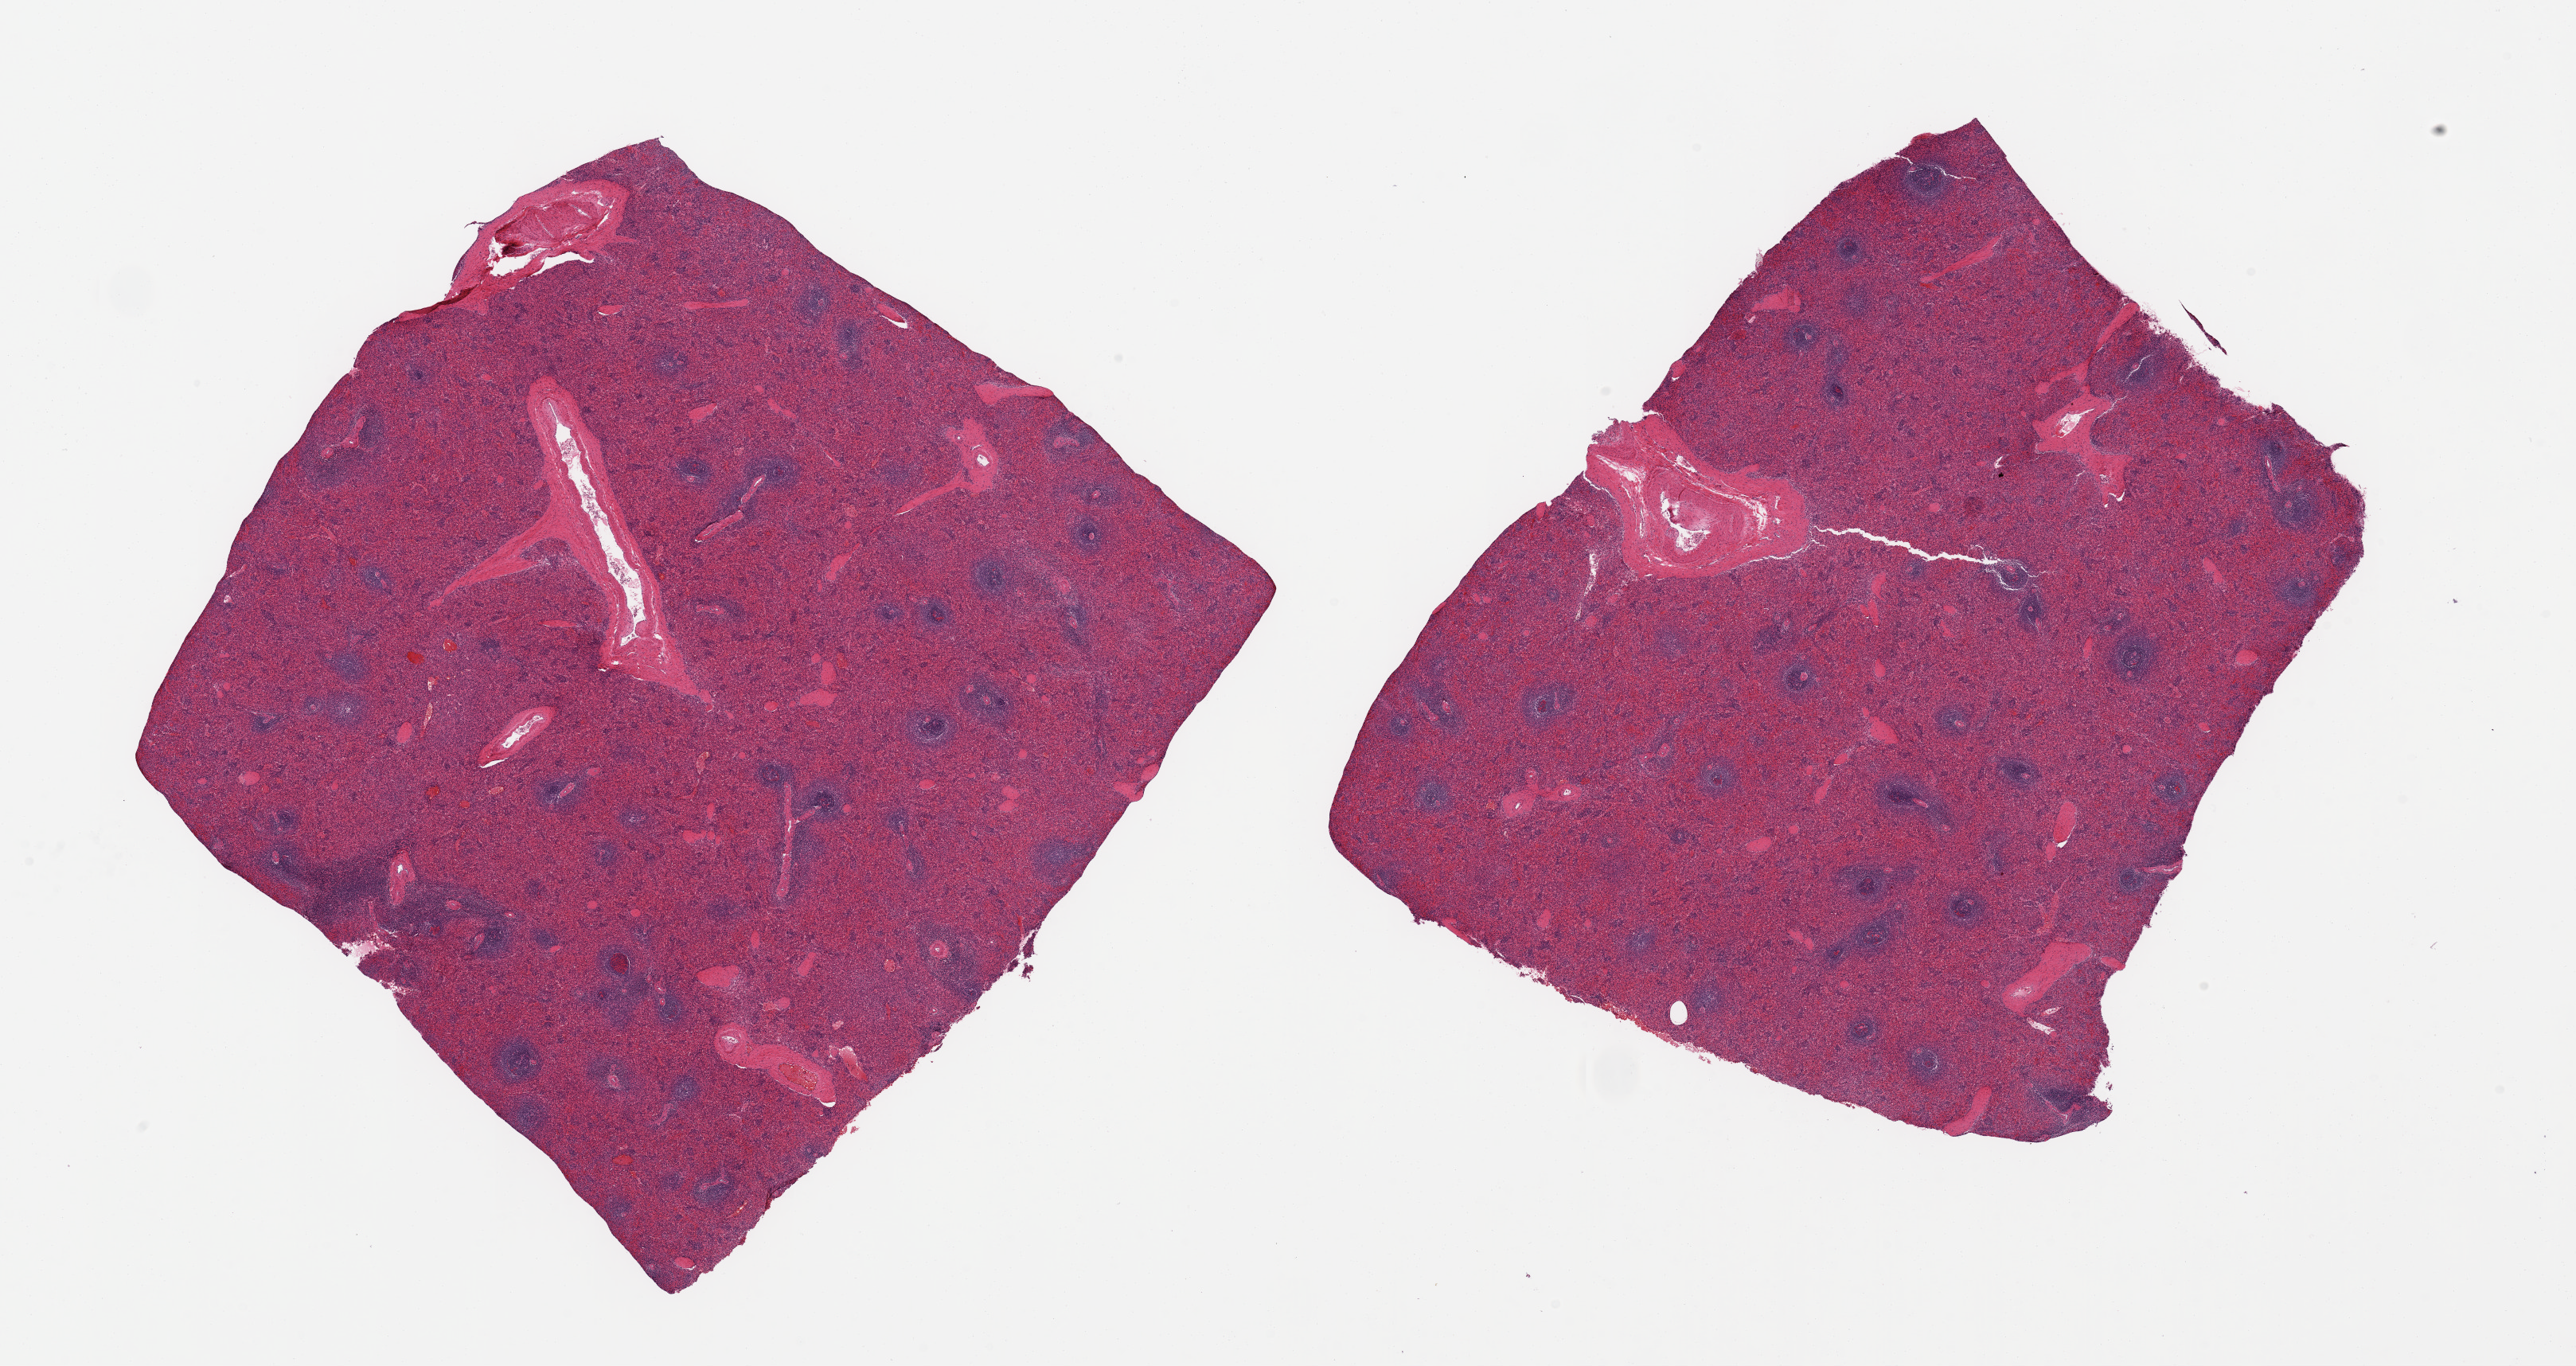
Haematoxylin and eosin whole-slide image, brightfield, shown as a low-resolution overview of the whole scanned area (about 25.6 x 13.6 mm); PAXgene-fixed, paraffin-embedded tissue; section of spleen (target tissue); donor tissue sample. Donor sex: male.
Review note (as recorded): 2 pieces.